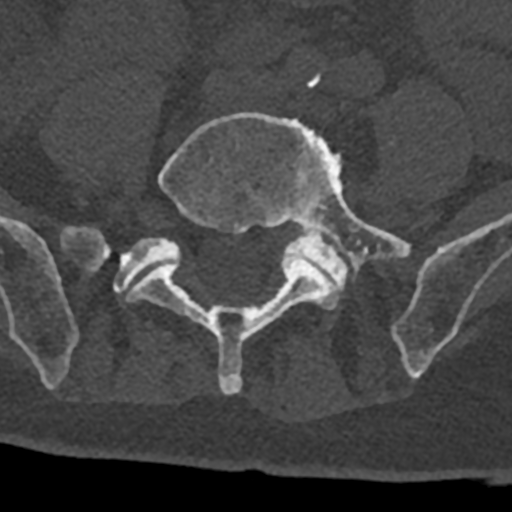
CT including the spine, one axial slice. Slice 193 of 797 in the series (ordered by position). Reconstruction kernel Br40s/3. 120 kVp. Bone window (W 1800 / L 400 HU). 512 × 512 image matrix, field of view 160 × 160 mm. Patient: male, 74 years. Case-level facts recorded for this patient, not image findings: primary cancer: renal.
Structures marked on this image (semi-automatic segmentation, software-assisted and operator-edited):
- L5 vertebra: bounding box [x1, y1, x2, y2] px = [126, 112, 411, 394]